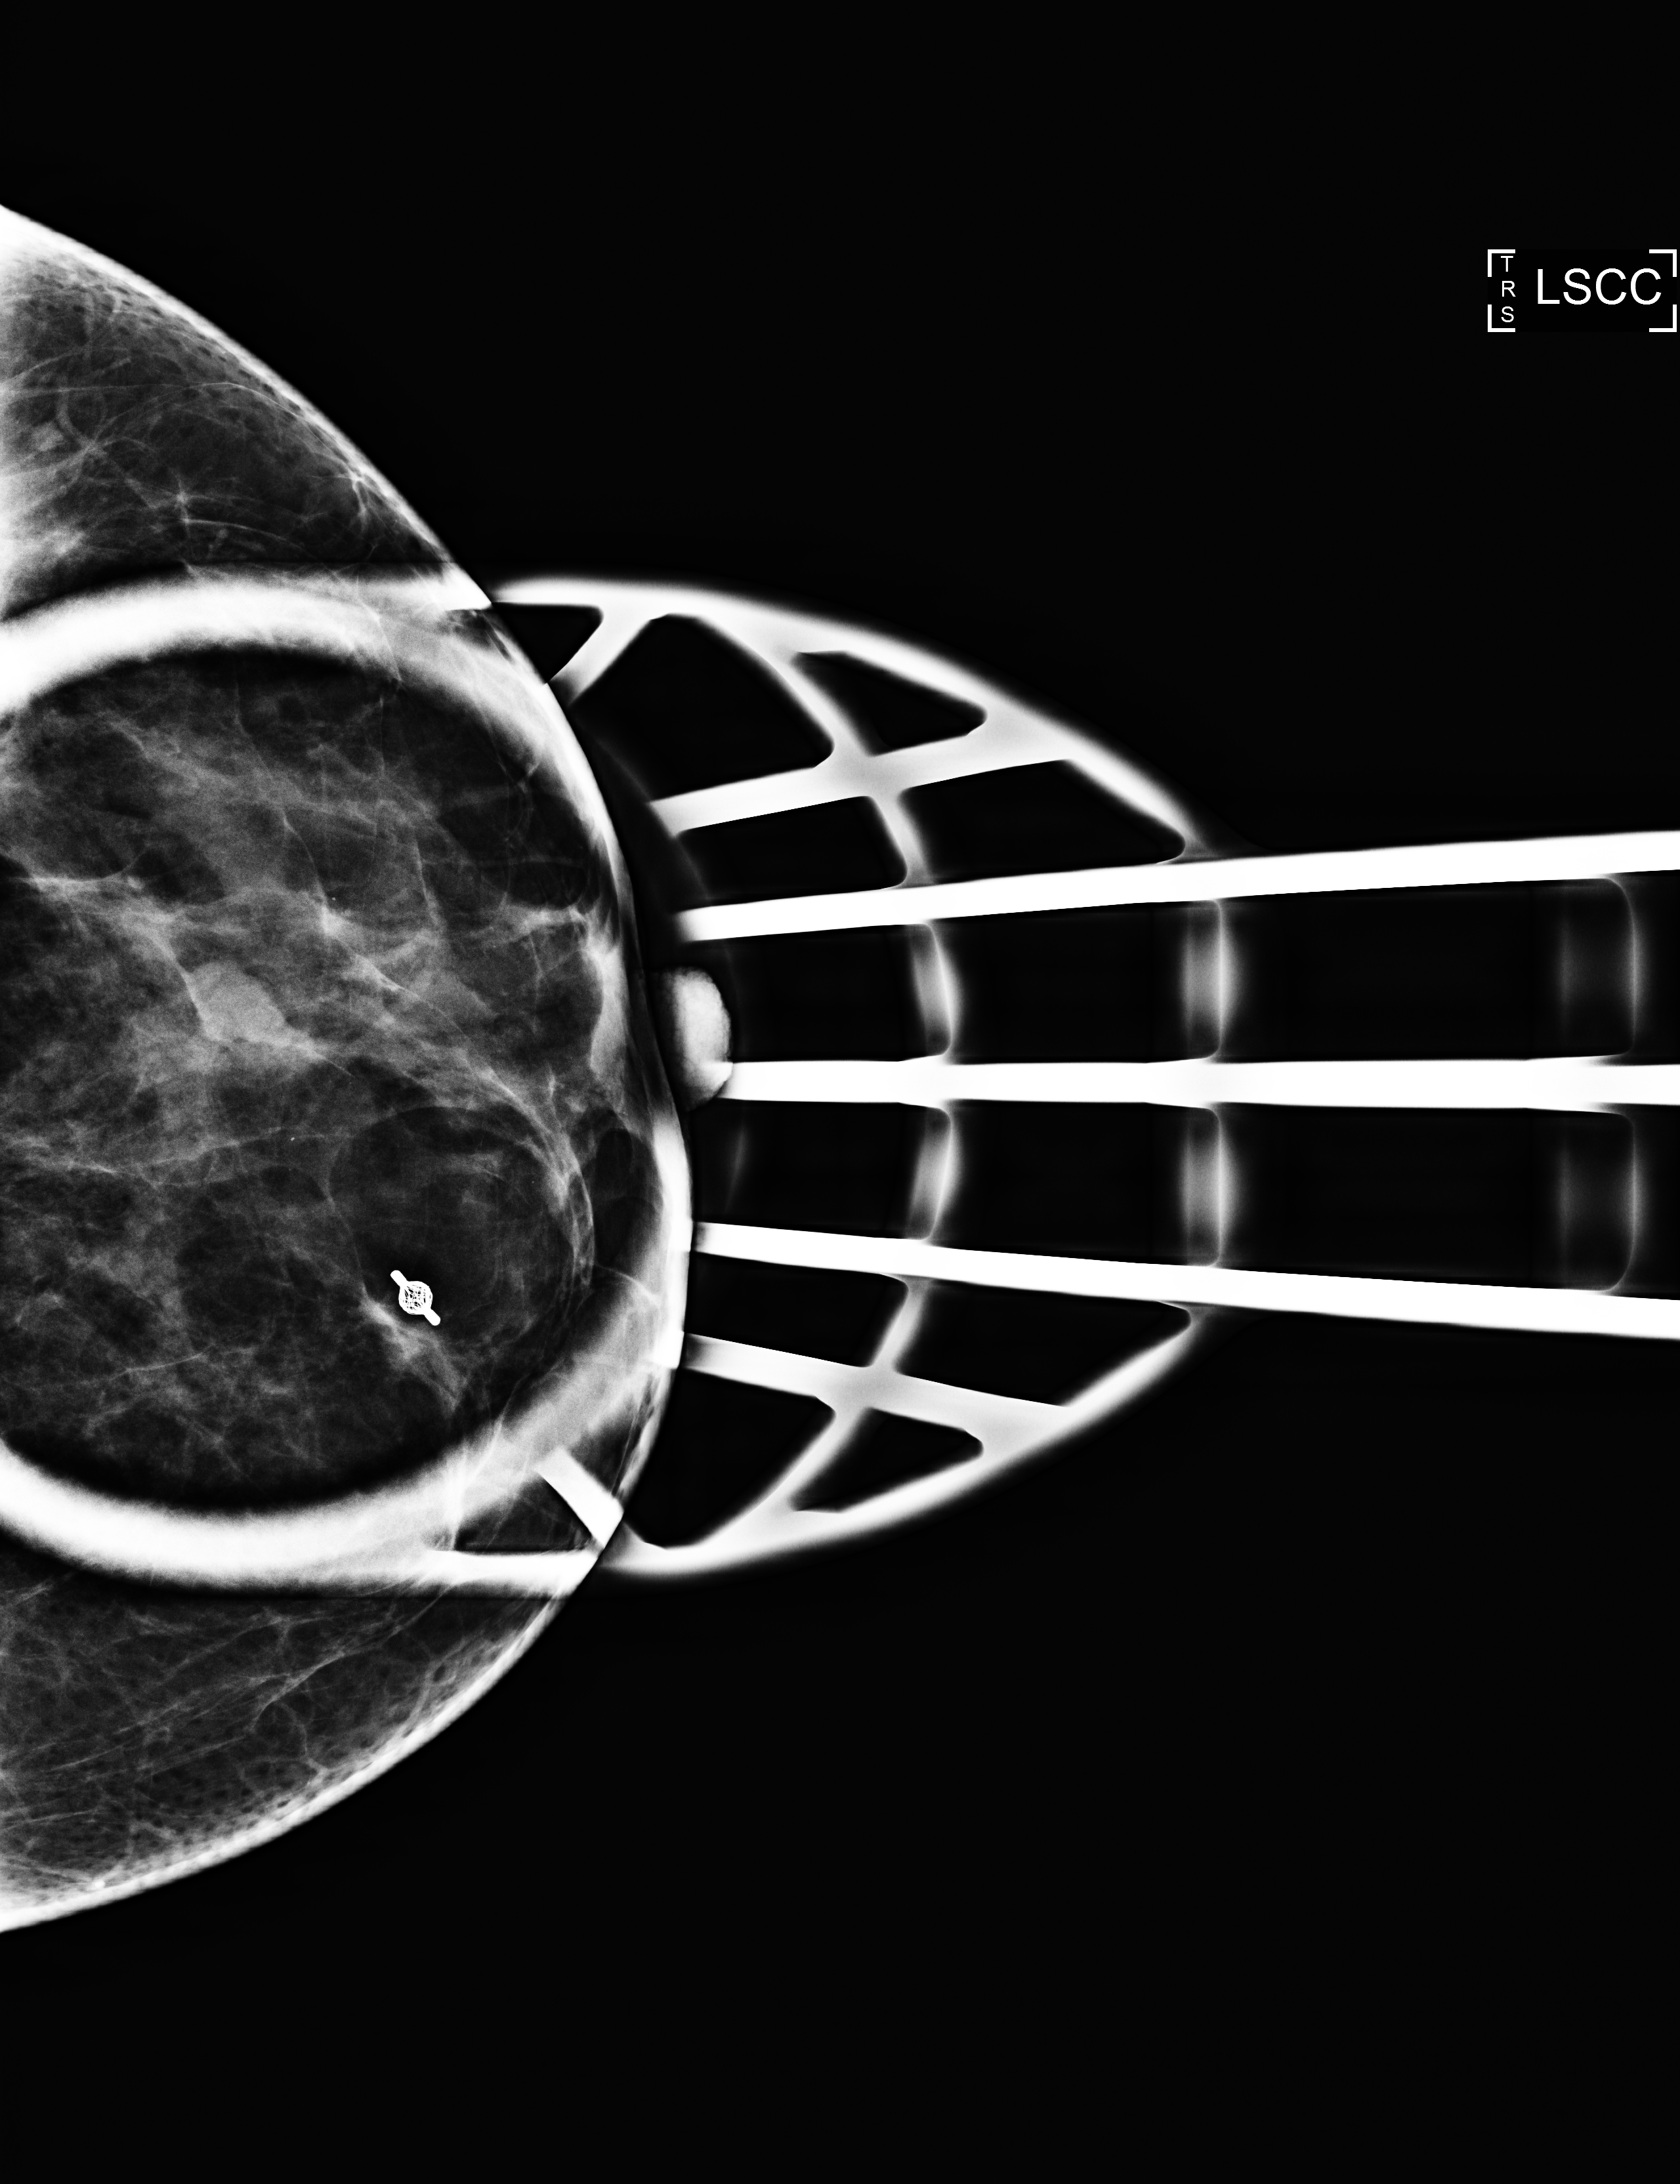
Additional (diagnostic) view. Patient: female, 42 years.
Image type: full-field digital mammogram. Breast: left. Projection: cranio-caudal projection, spot compression.